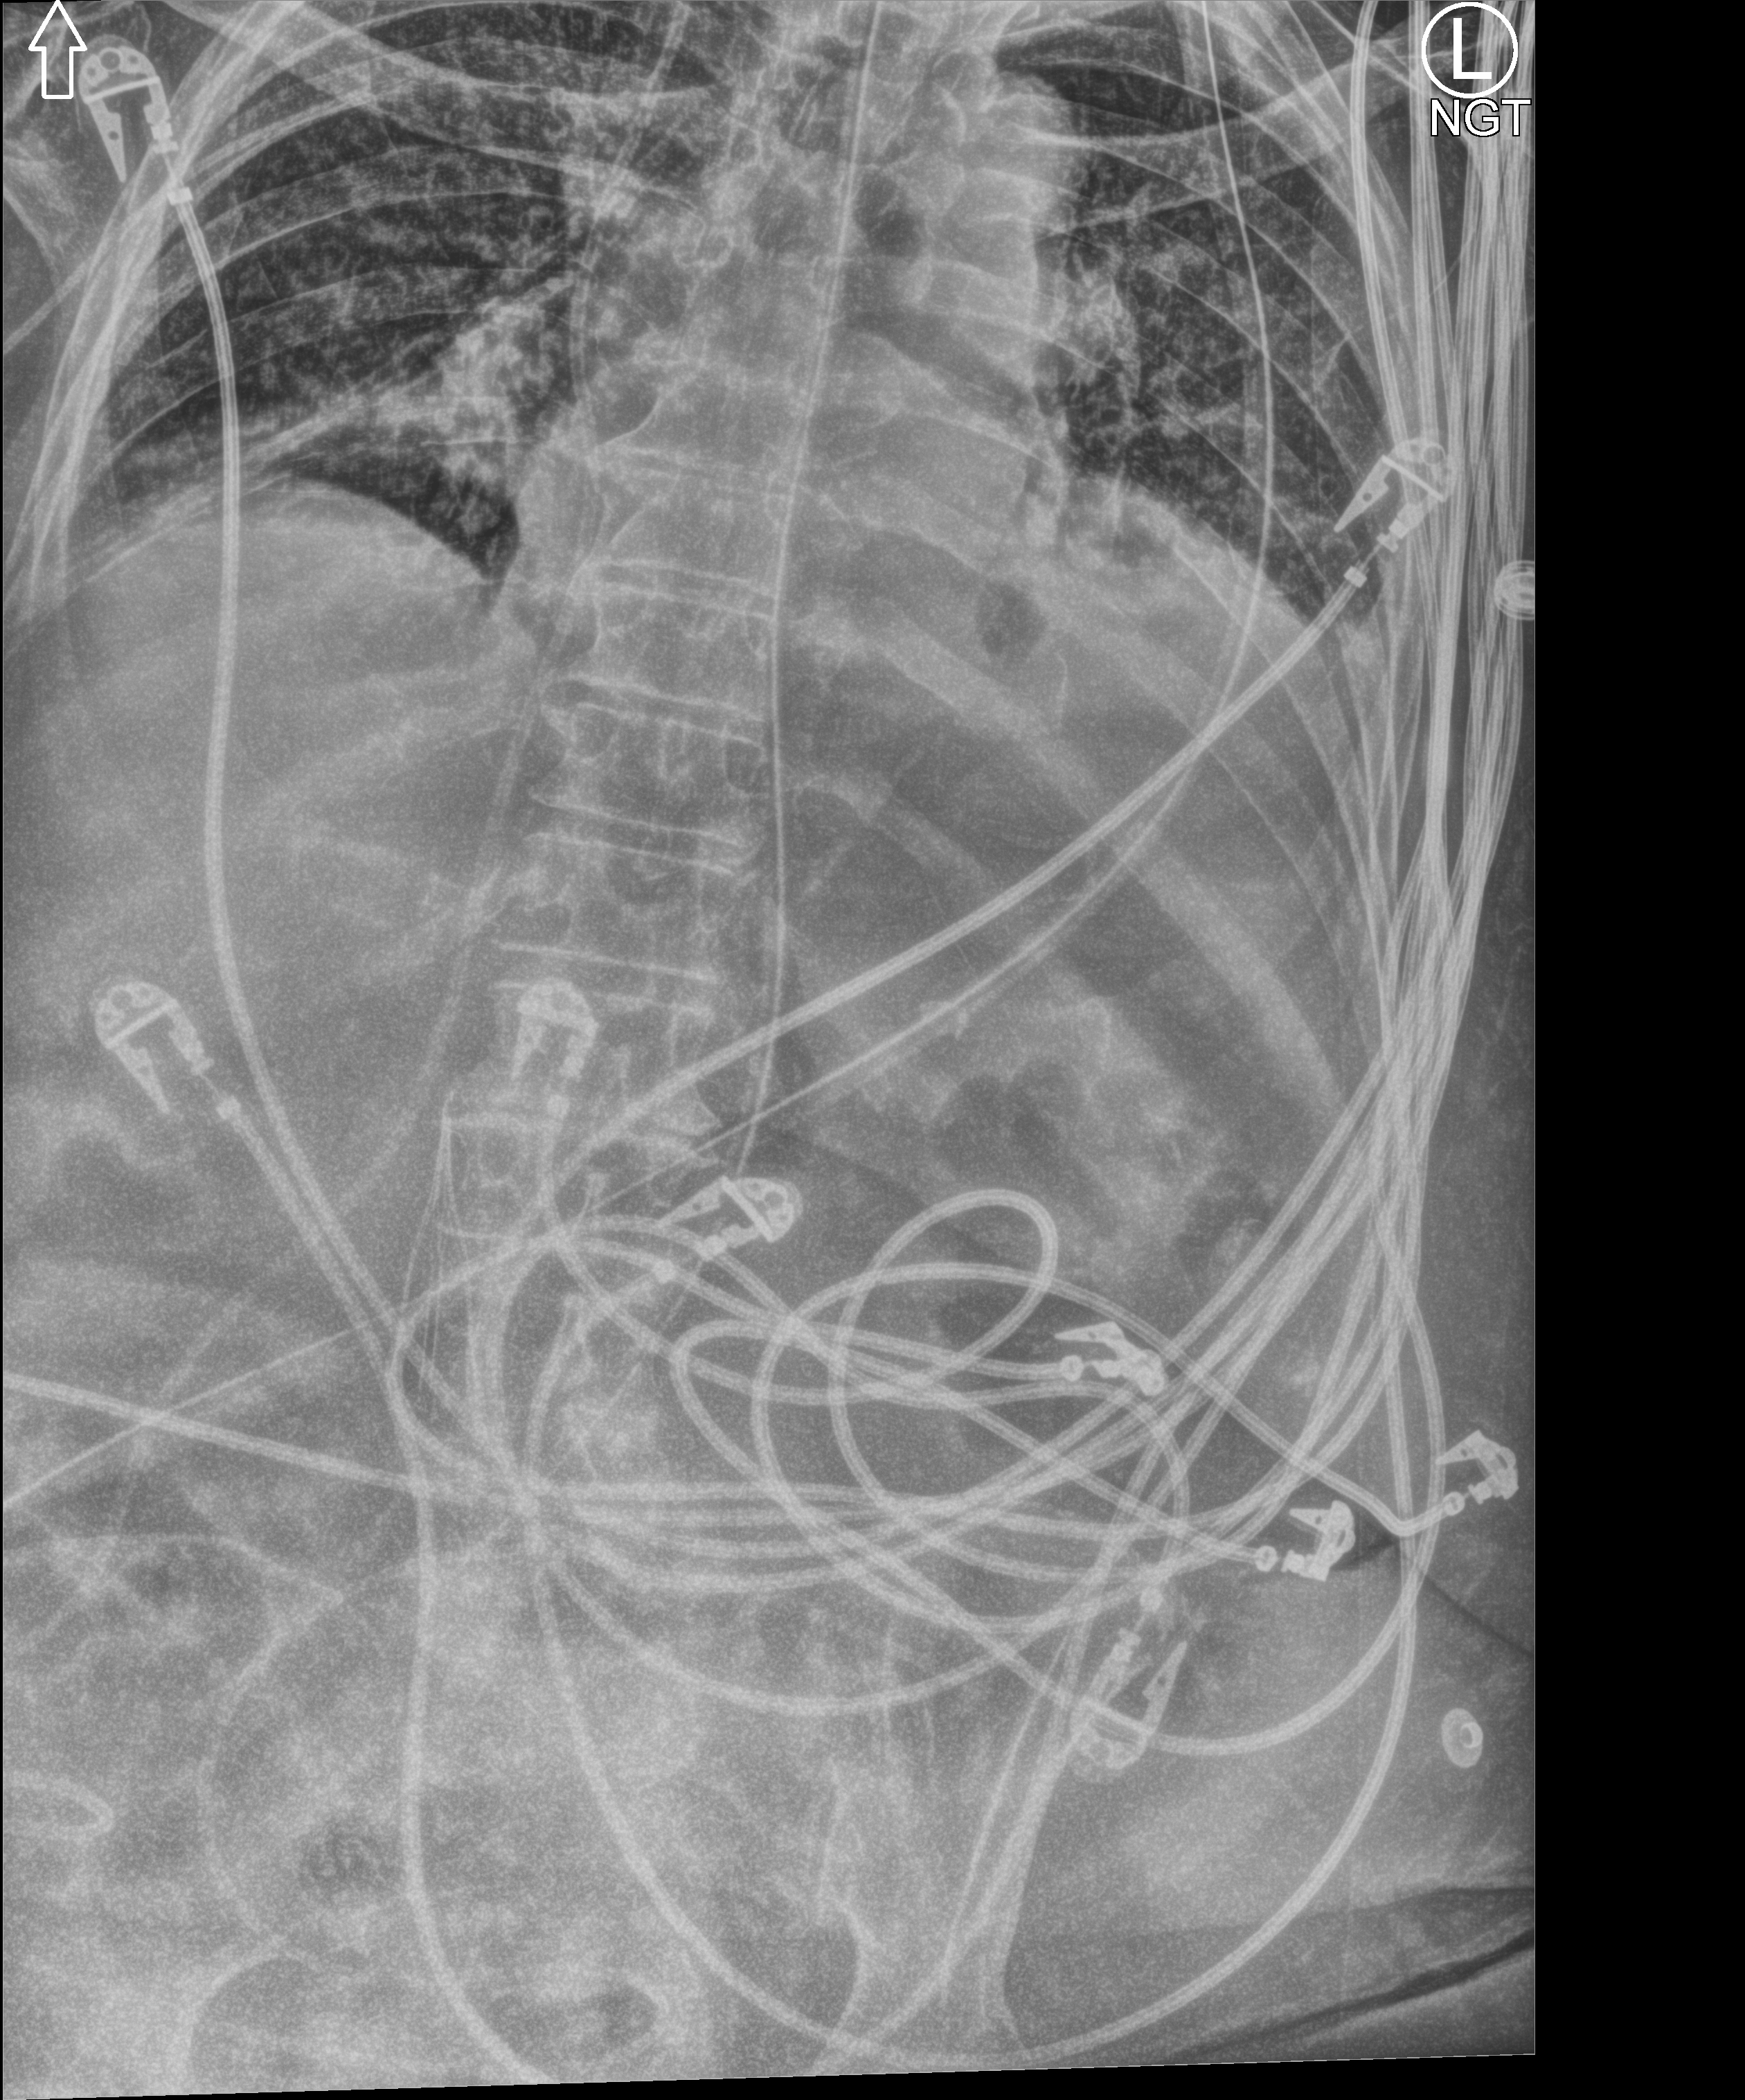
Abdomen X-ray (portable). Female patient hospitalised with COVID-19, age 75–90 years.
Admission-level facts for this patient (not findings on this image; timing relative to this image not recorded):
- admitted to intensive care during this hospital stay: yes